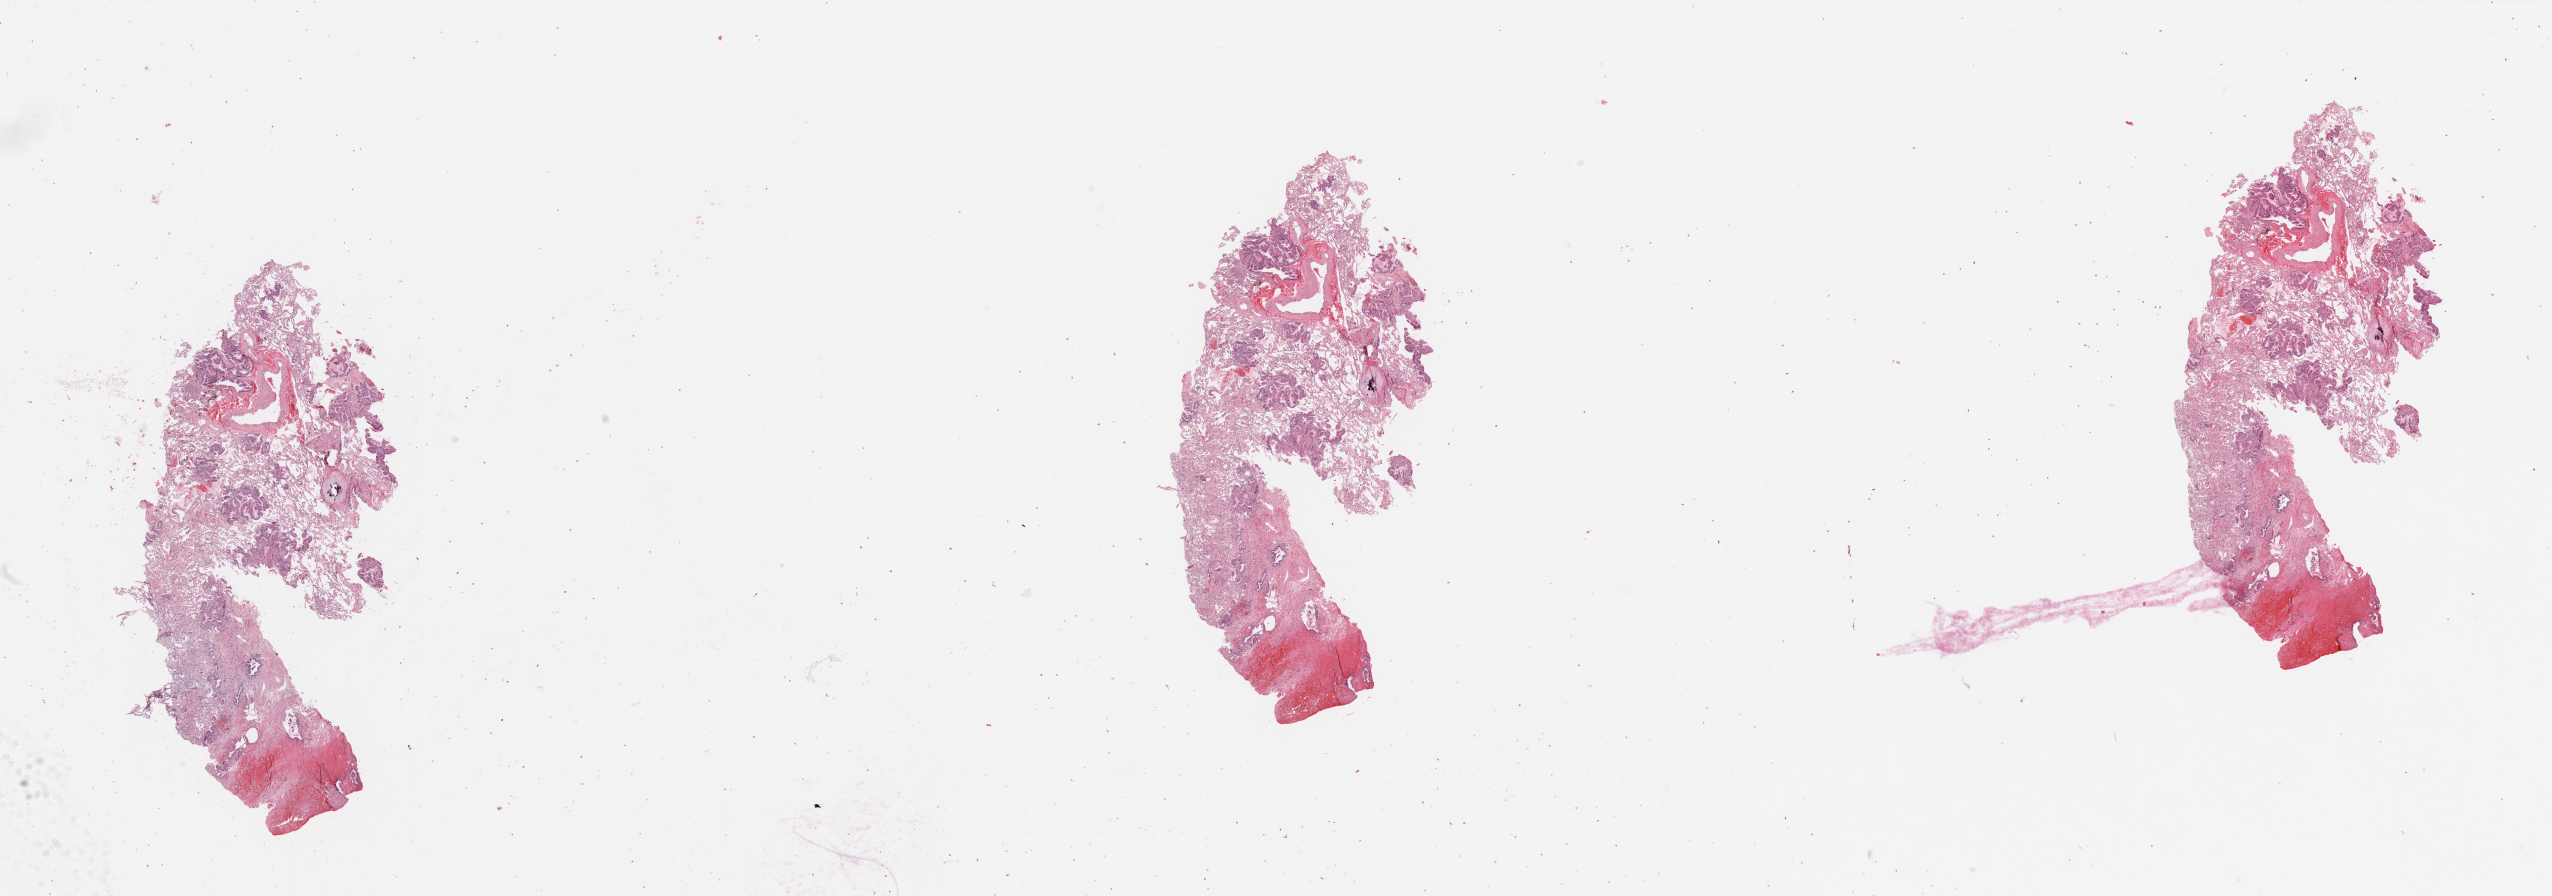
H&E whole-slide image, whole scanned area (about 40.4 x 14.2 mm, acquisition: 20x scan) shown as a low-resolution overview; tumour tissue sample, lung. Patient: male, age 66 years. Histologic grade: G2 (moderately differentiated).
Histologic diagnosis: Adenocarcinoma, NOS. AJCC pathologic stage: IB. Primary tumour site (as recorded): left lower lobe.